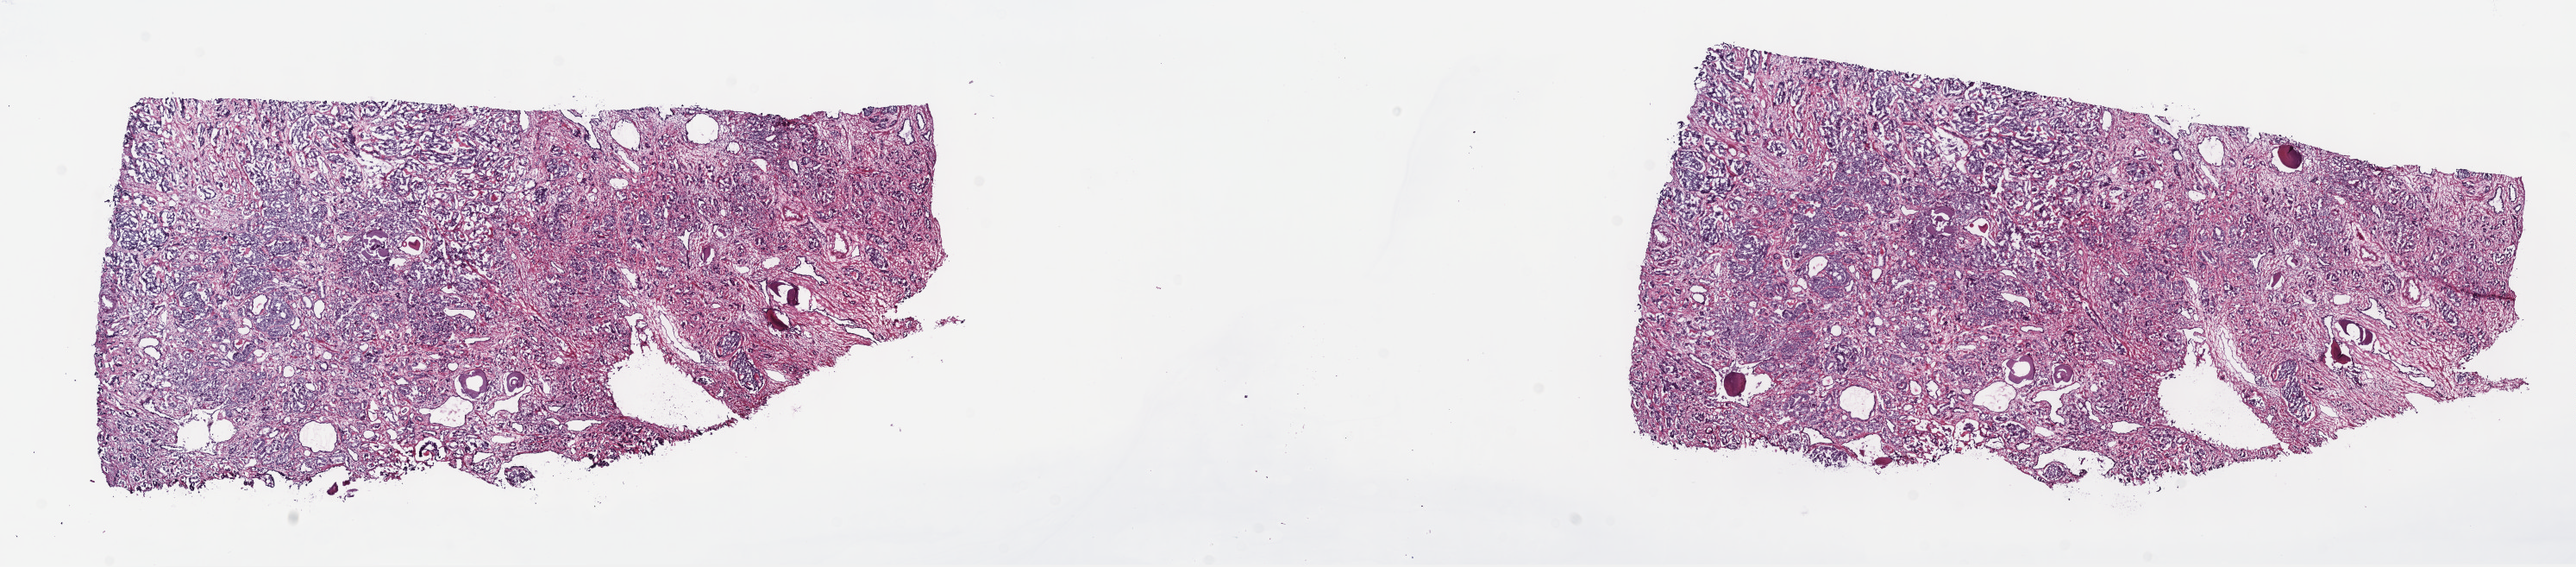
H&E-stained whole-slide image, shown as a low-resolution overview of the whole scanned area (about 24.2 x 5.3 mm, acquisition: 40x scan), frozen section from the top of the tissue portion, sample: primary tumour, prostate. Patient: male, age at initial diagnosis 64 years.
Histologic diagnosis: Adenocarcinoma, NOS (prostate gland).